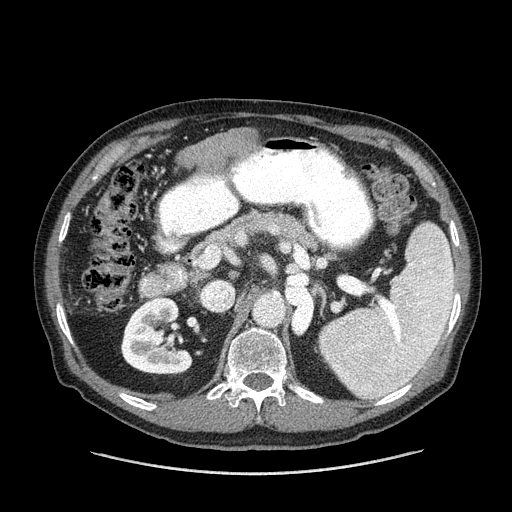
Contrast-enhanced abdominal CT (liver protocol), one axial slice. Slice 62 of 180 in the series (ordered by position). One of 2 acquisitions stored at this slice position. Soft-tissue window (W 400 / L 40 HU). 512 × 512 image matrix, field of view 420 × 420 mm. Case-level facts recorded for this patient, not image findings: diagnosis: hepatocellular carcinoma (patient treated with transarterial chemoembolisation; whether this scan precedes or follows treatment is not stated here); TNM stage (as recorded): Stage-II; Child-Pugh class: A; tumour nodularity: multinodular; tumour size: 2.8 cm.
Outlined on this slice (semi-automatic segmentation, software-assisted and operator-edited):
- liver parenchyma outside the tumour (the mass and vessels are separate outlines, so this box may not span the whole liver): bounding box [x1, y1, x2, y2] px = [182, 132, 244, 164]